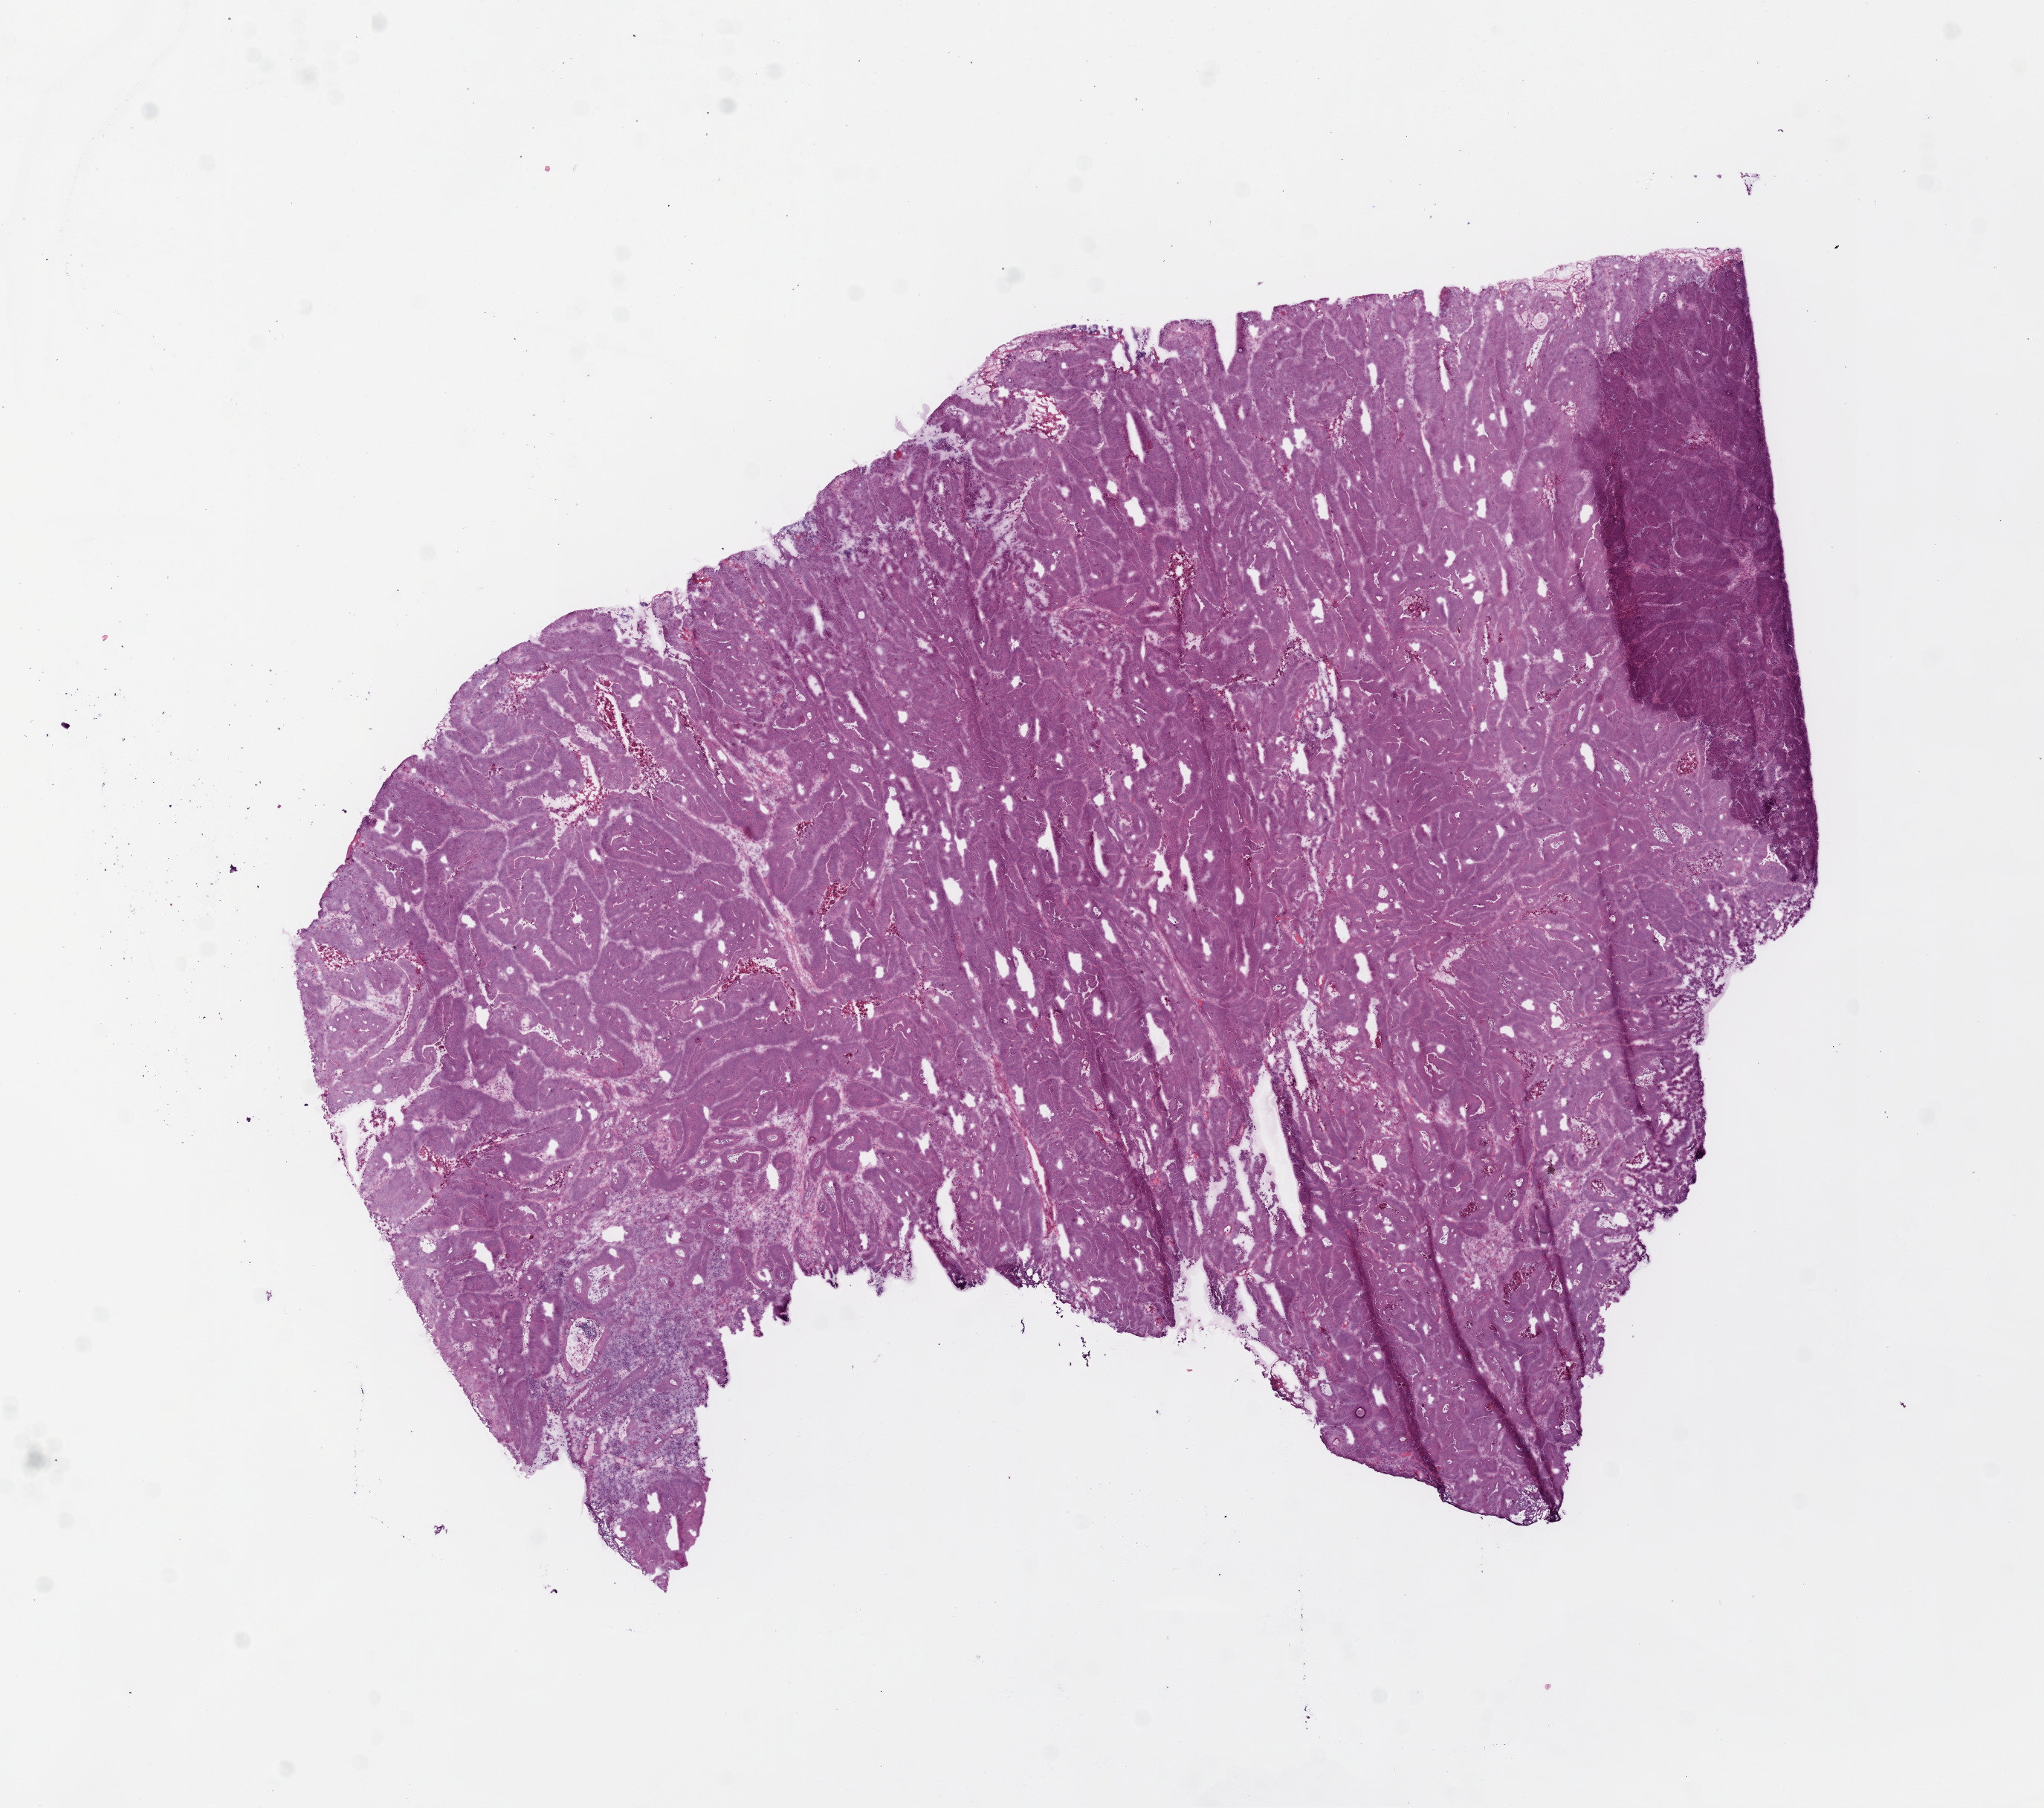
Digitized H&E-stained tissue section (whole slide) — shown as a low-resolution overview of the whole scanned area (about 11.0 x 9.8 mm, from a 20x scan); frozen section from the bottom of the tissue portion; primary tumour sample from the colon. Patient: female, age at initial diagnosis 77 years. Composition of this section per pathologist review: tumour cells 93%, tumour nuclei 85%, normal cells 0%, stromal cells 2%, necrosis 5%.
AJCC pathologic stage: III (5th edition). Pathologic diagnosis: Adenocarcinoma, NOS (cecum).